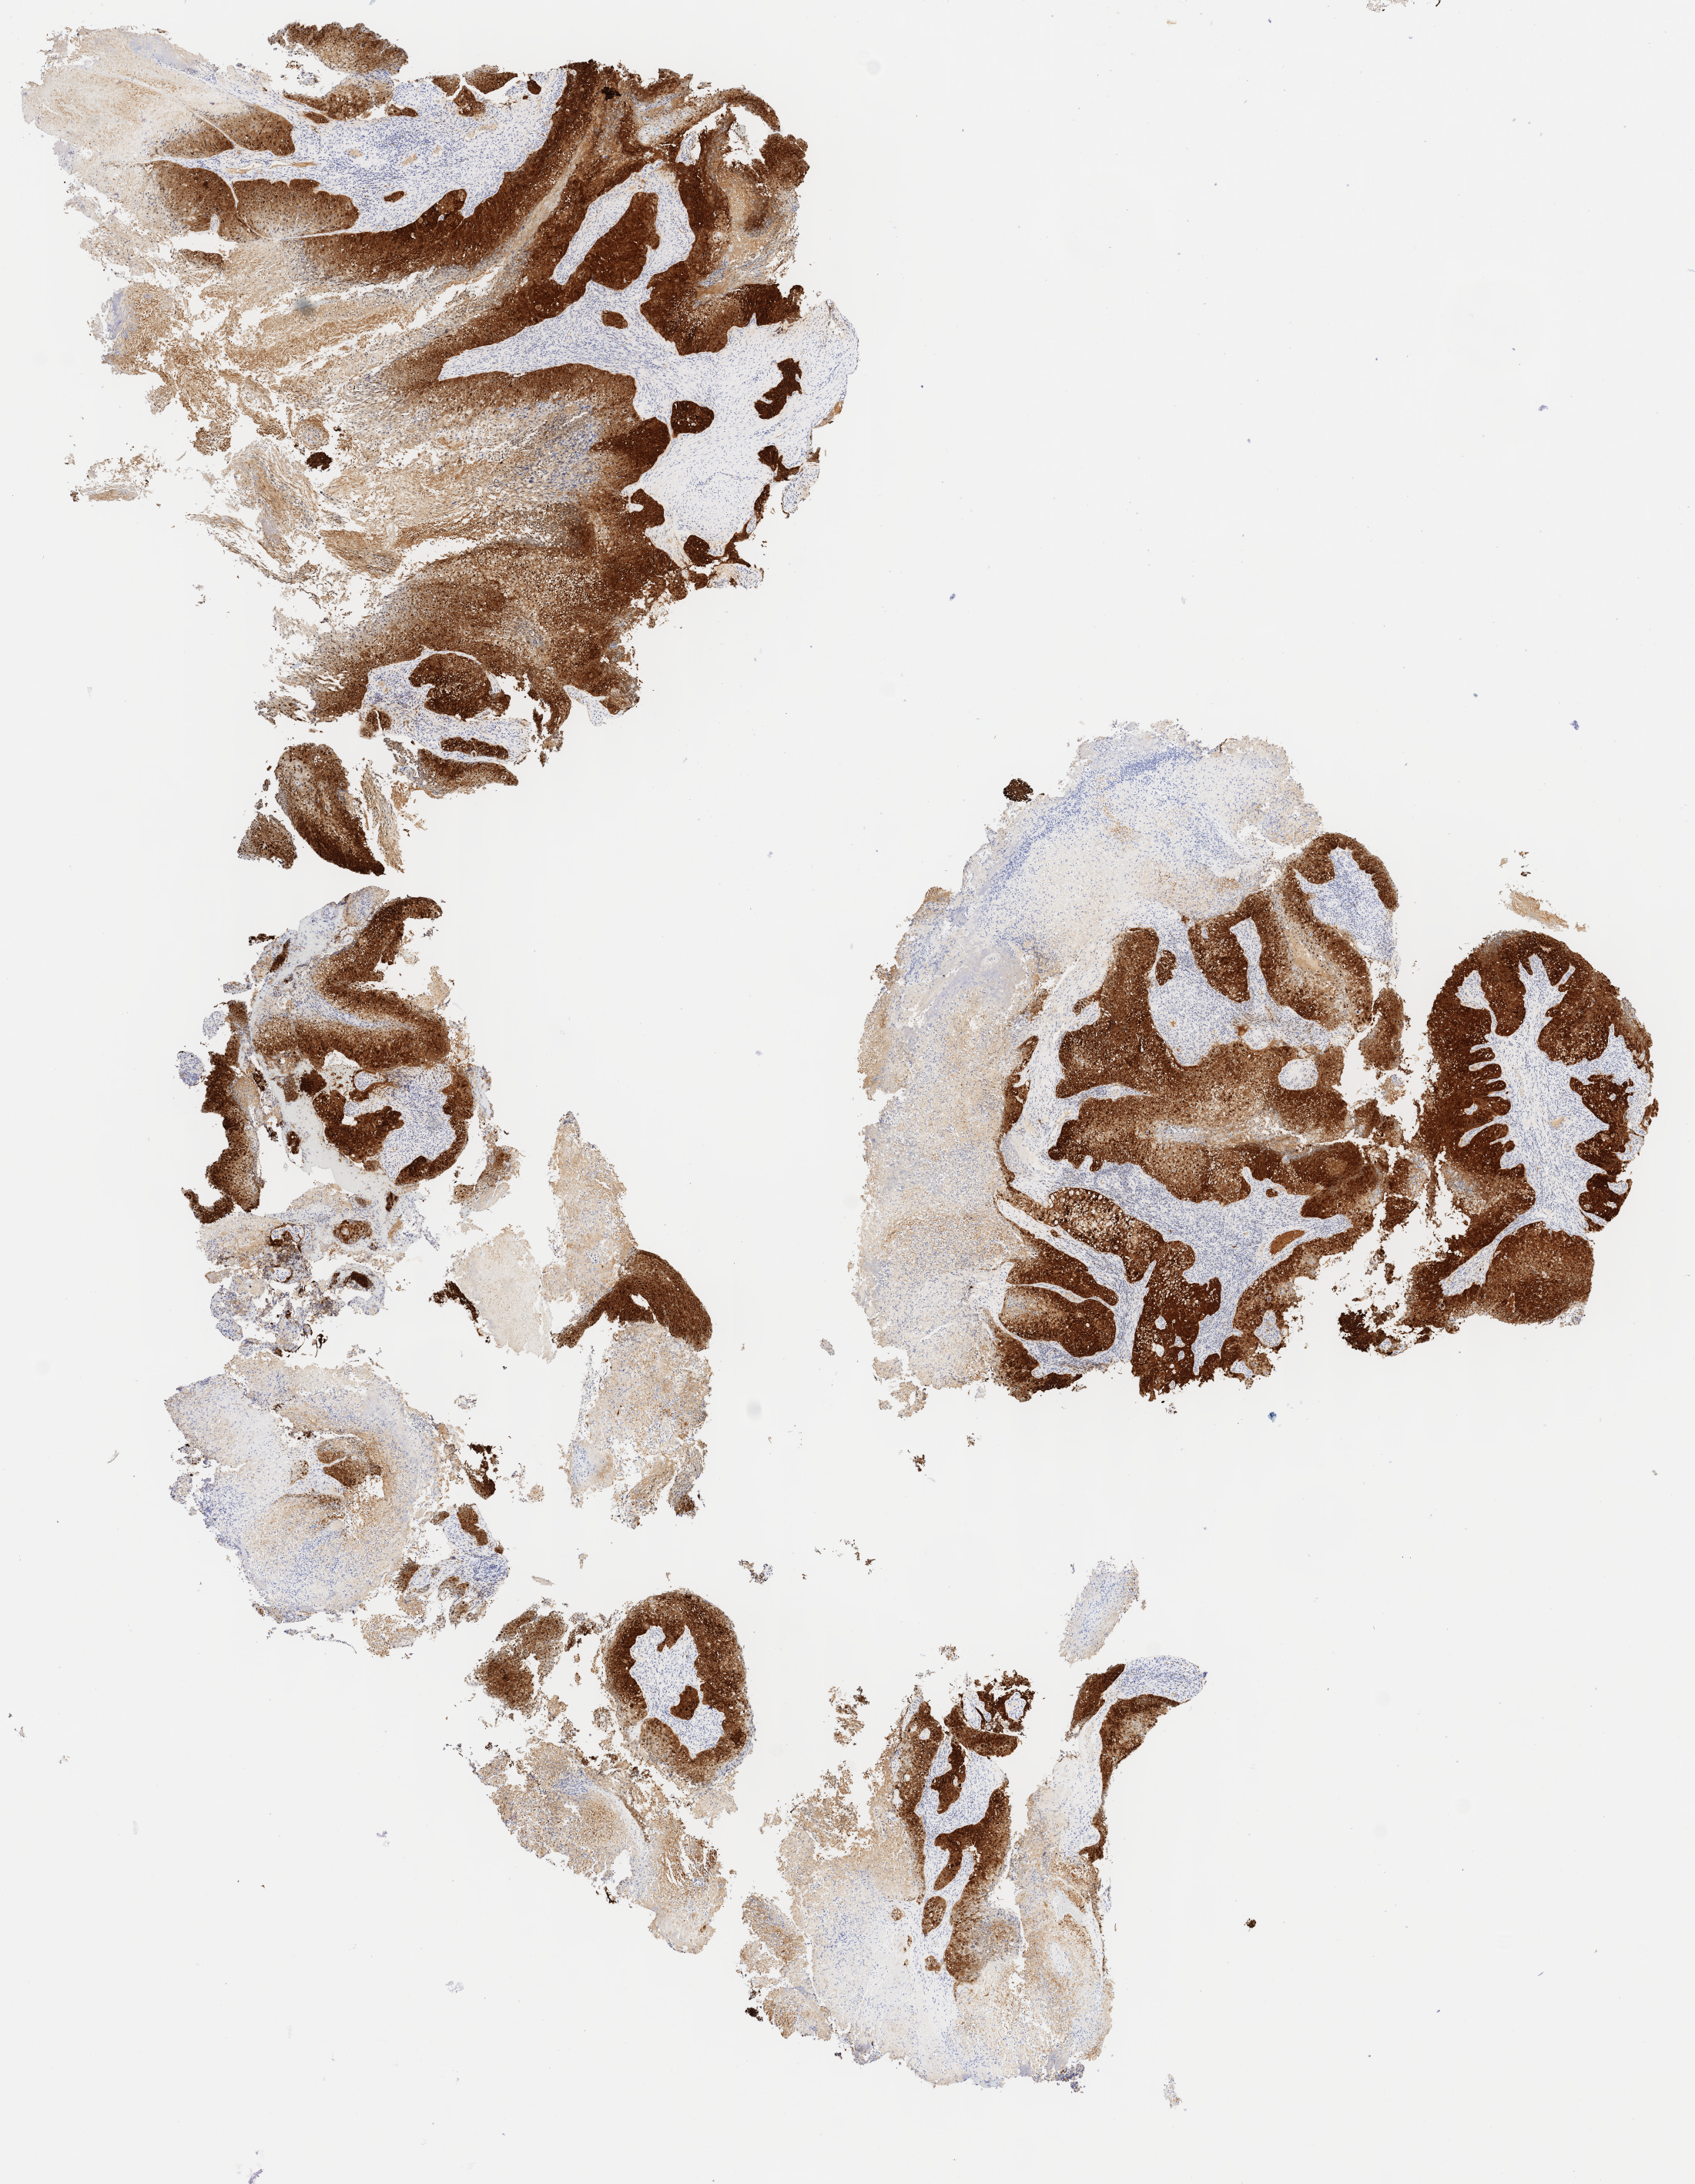
Whole-slide image, immunohistochemical stain for p16 (p16INK4a), low-resolution overview of the scanned area, about 8.8 x 11.3 mm. Tumor tissue. Anatomic site: cervix. Patient female; 41 years old.
Diagnosis: Squamous cell carcinoma, large cell, nonkeratinizing, NOS.